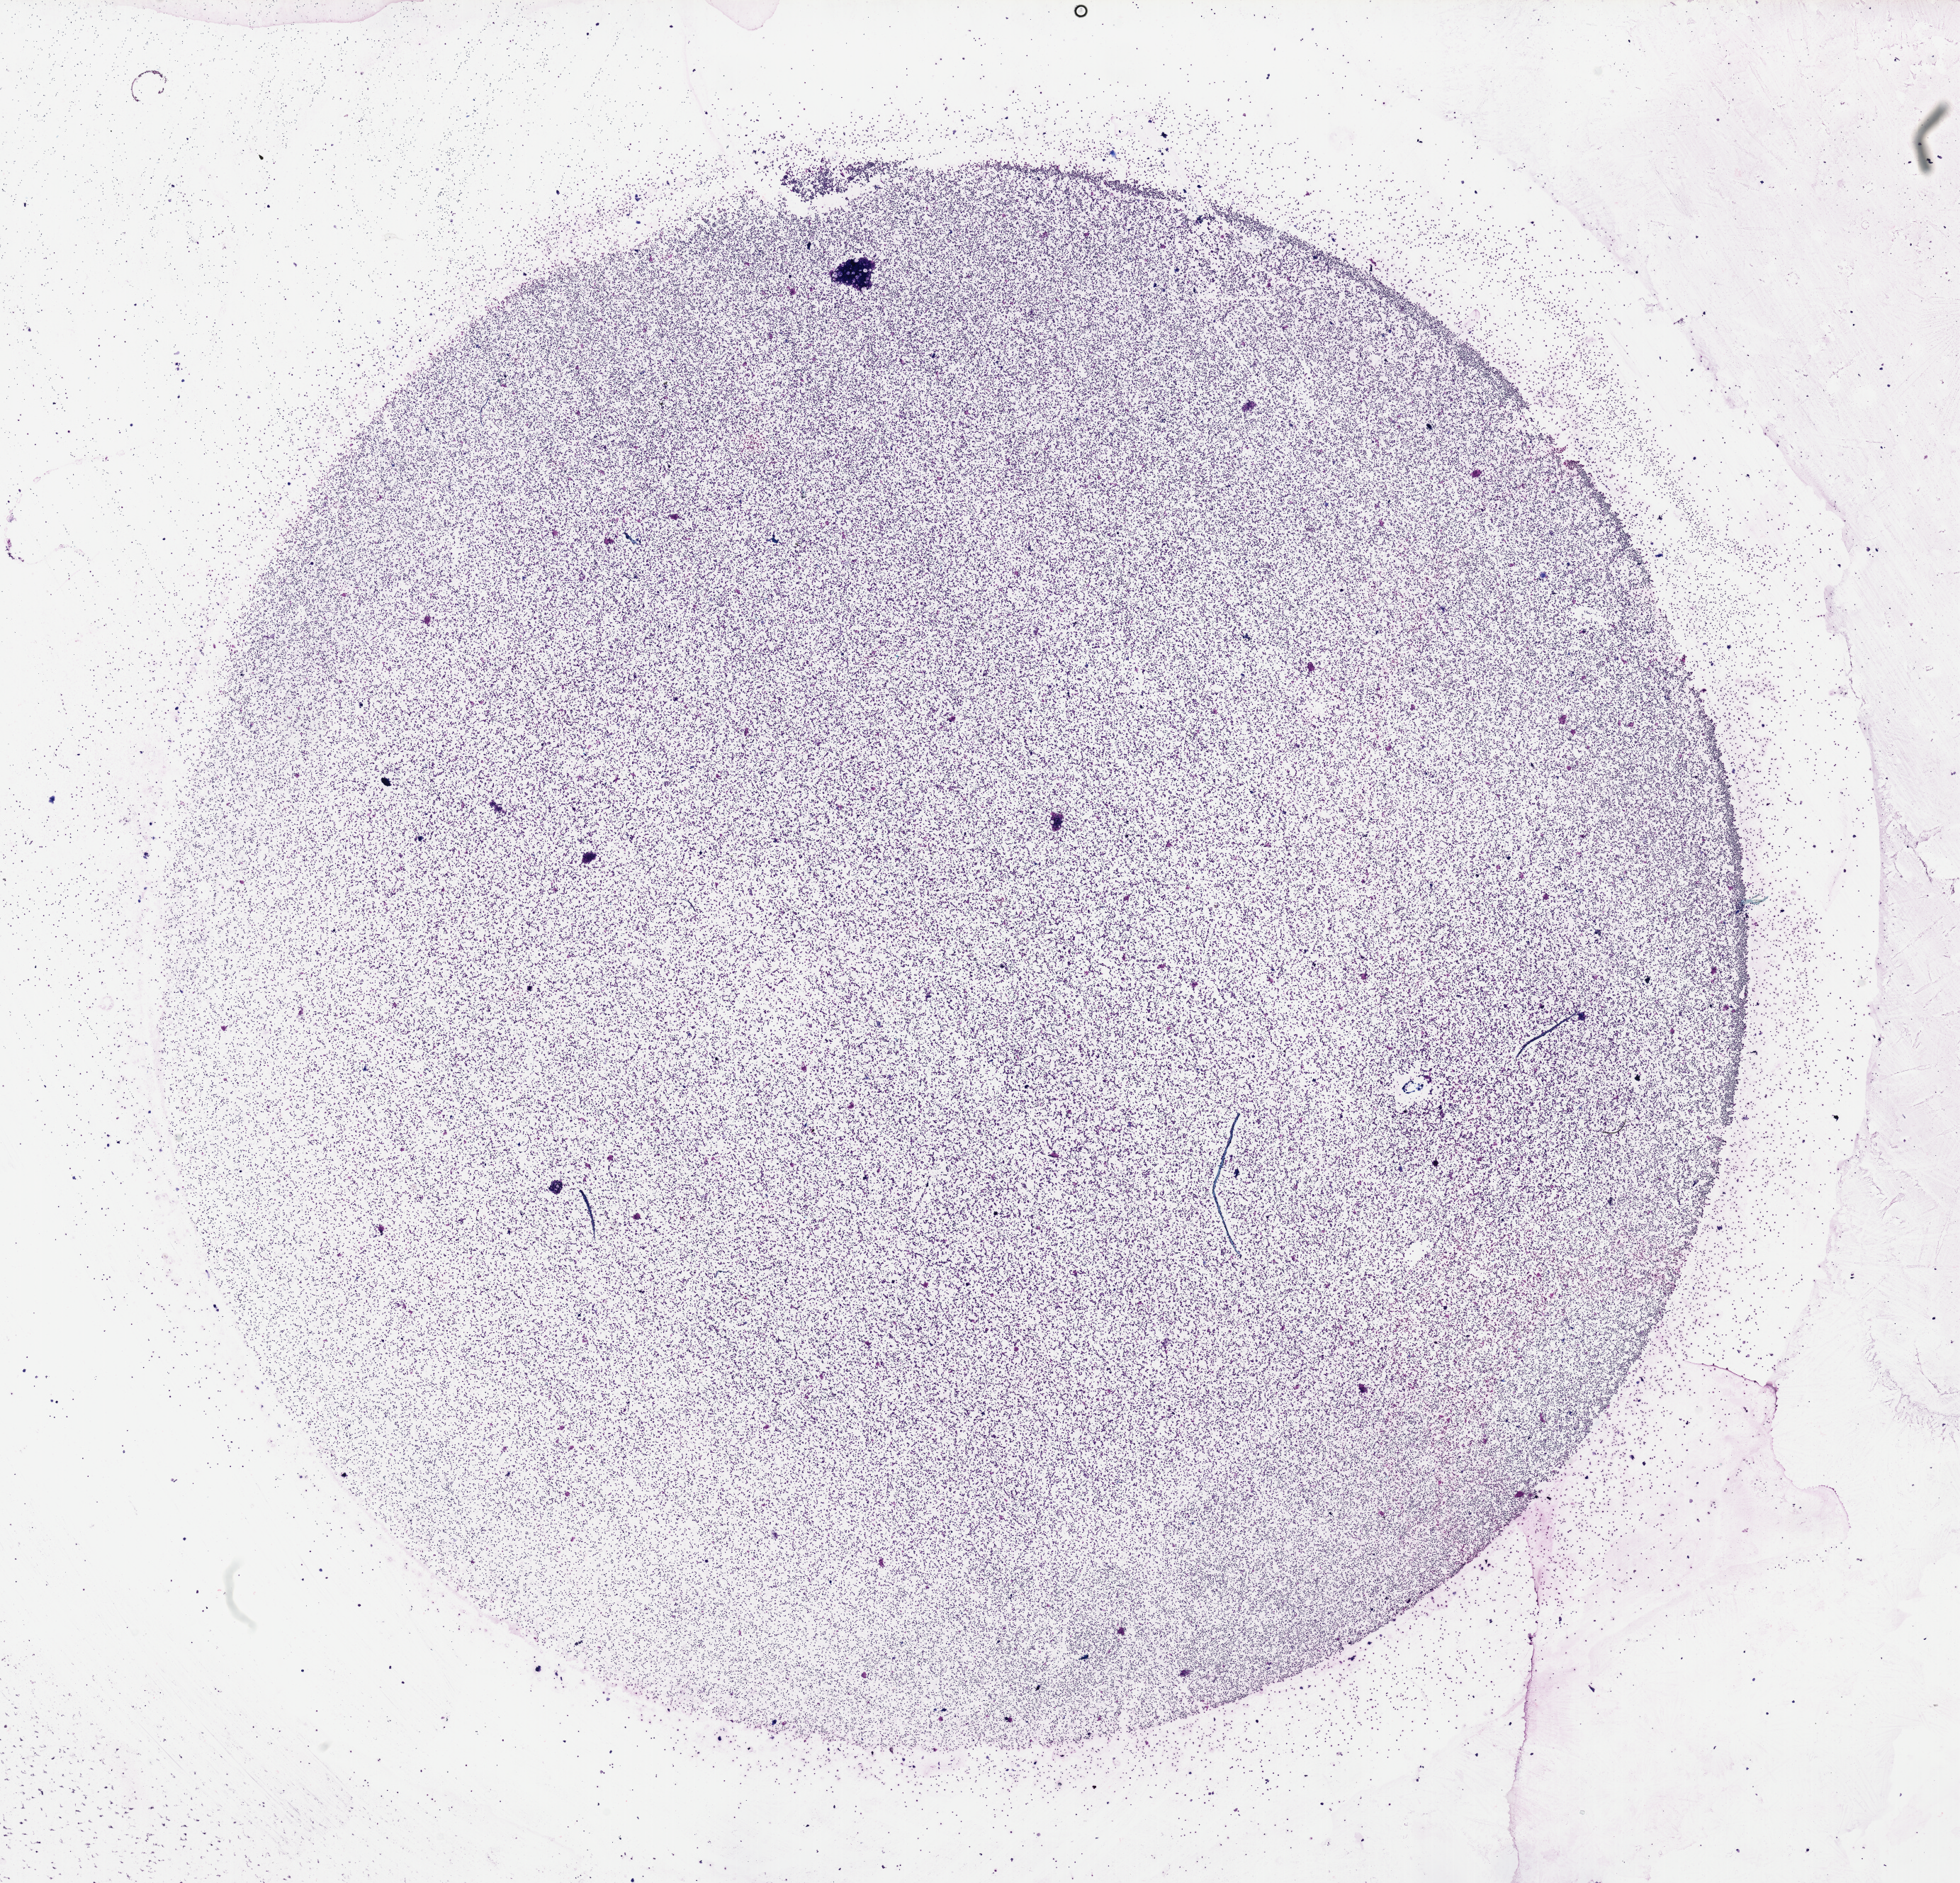
Digitized H&E tissue section (whole slide), low-resolution overview of the scanned area, about 21.8 x 21.0 mm (slide scanned at 40x). Bone marrow (leukaemic) sample. Male, 68 y/o.
Diagnosis: Acute Myeloid Leukemia.